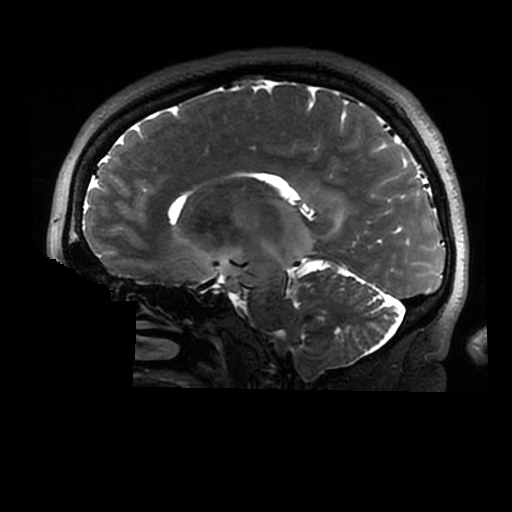
Brain MRI from a brain-tumour surgery series, one sagittal slice; position 172 of 320 along the scan axis; 512 × 512 image matrix. Case-level facts recorded for this patient, not image findings: histopathology: Astrocytoma; WHO grade: 2; IDH mutation: yes.
Structures marked on this image (manually delineated by an expert):
- tumour: bounding box <202,200,315,292> (left, top, right, bottom; pixels)